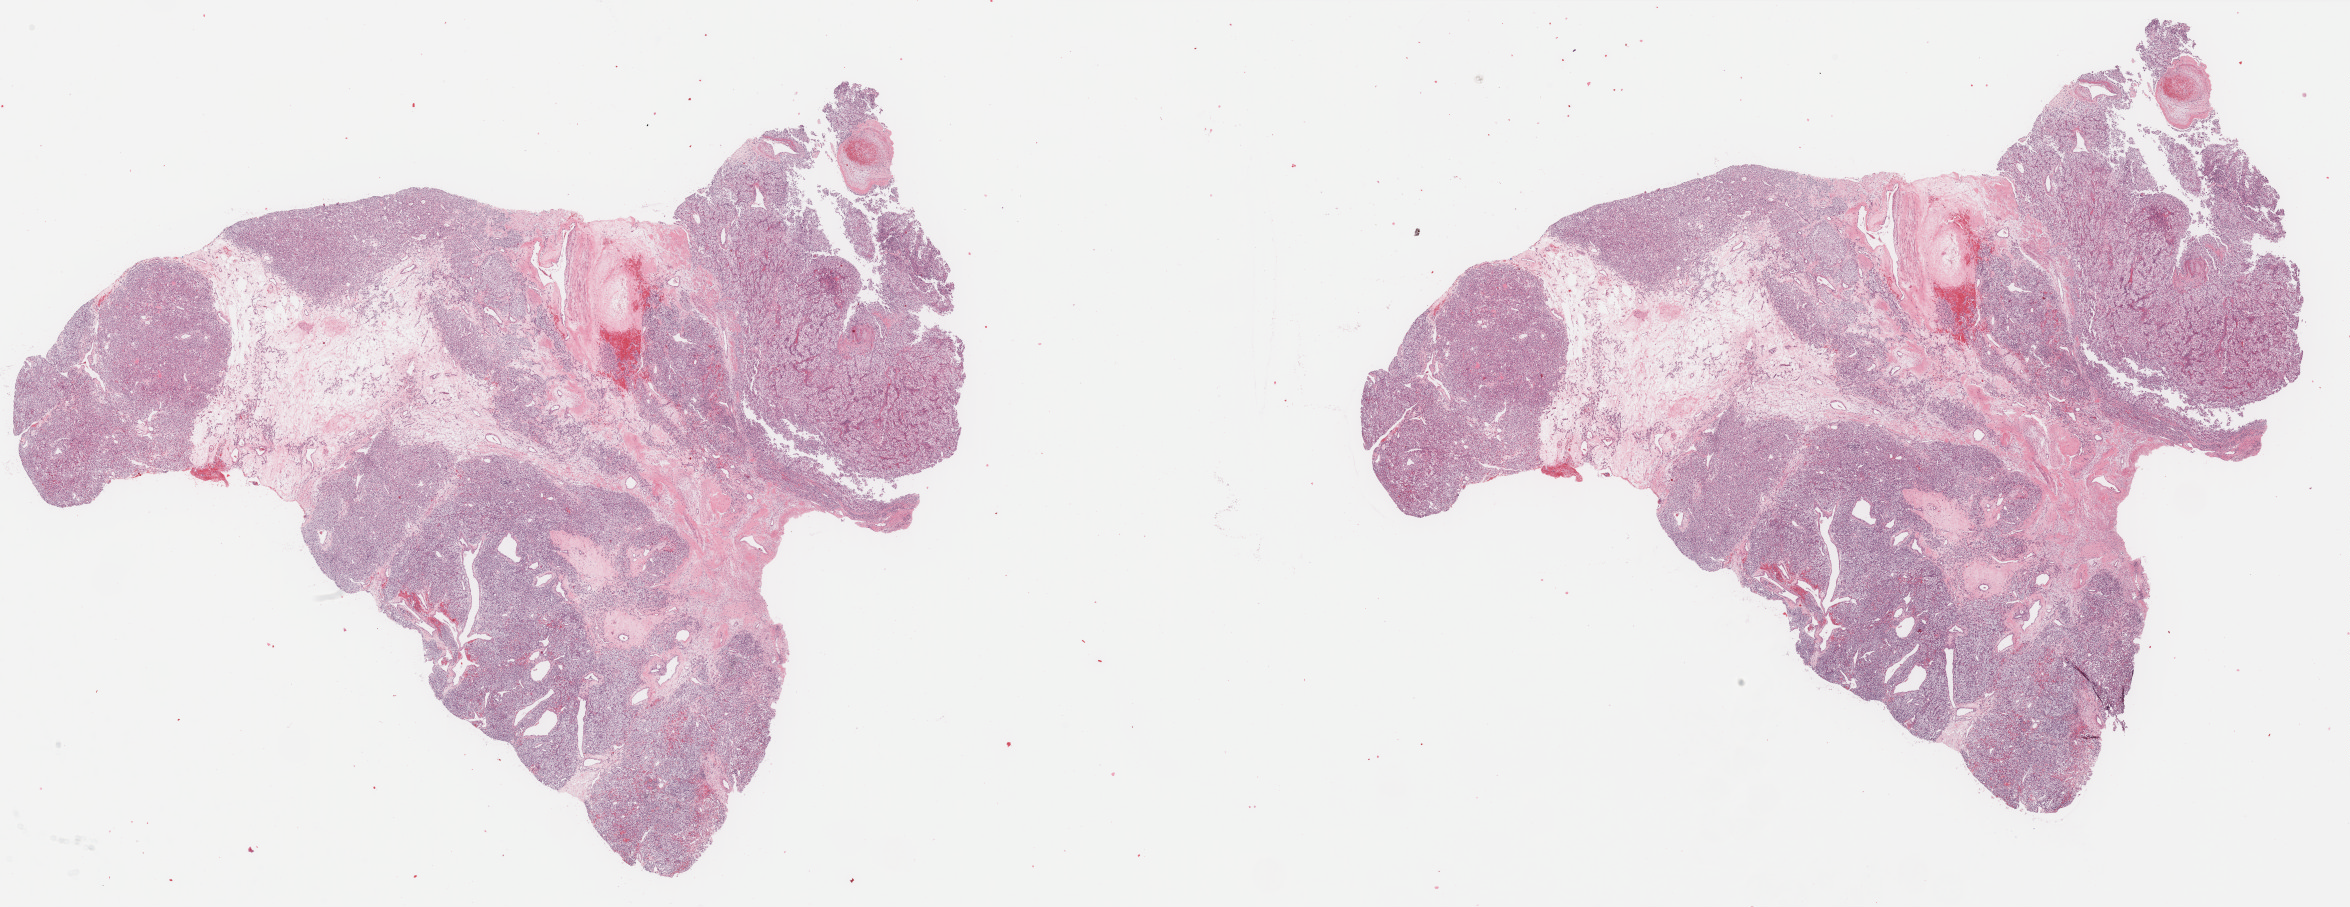
H&E whole-slide image — whole scanned area (about 37.2 x 14.4 mm) shown as a low-resolution overview, formalin-fixed paraffin-embedded (FFPE) diagnostic section, sample: primary tumour, kidney. Female, age 69 years at initial diagnosis. Histologic grade: G3 (poorly differentiated).
Diagnosis: Renal cell carcinoma, NOS. TNM: T2a N0 MX. AJCC pathologic stage: II (7th edition).